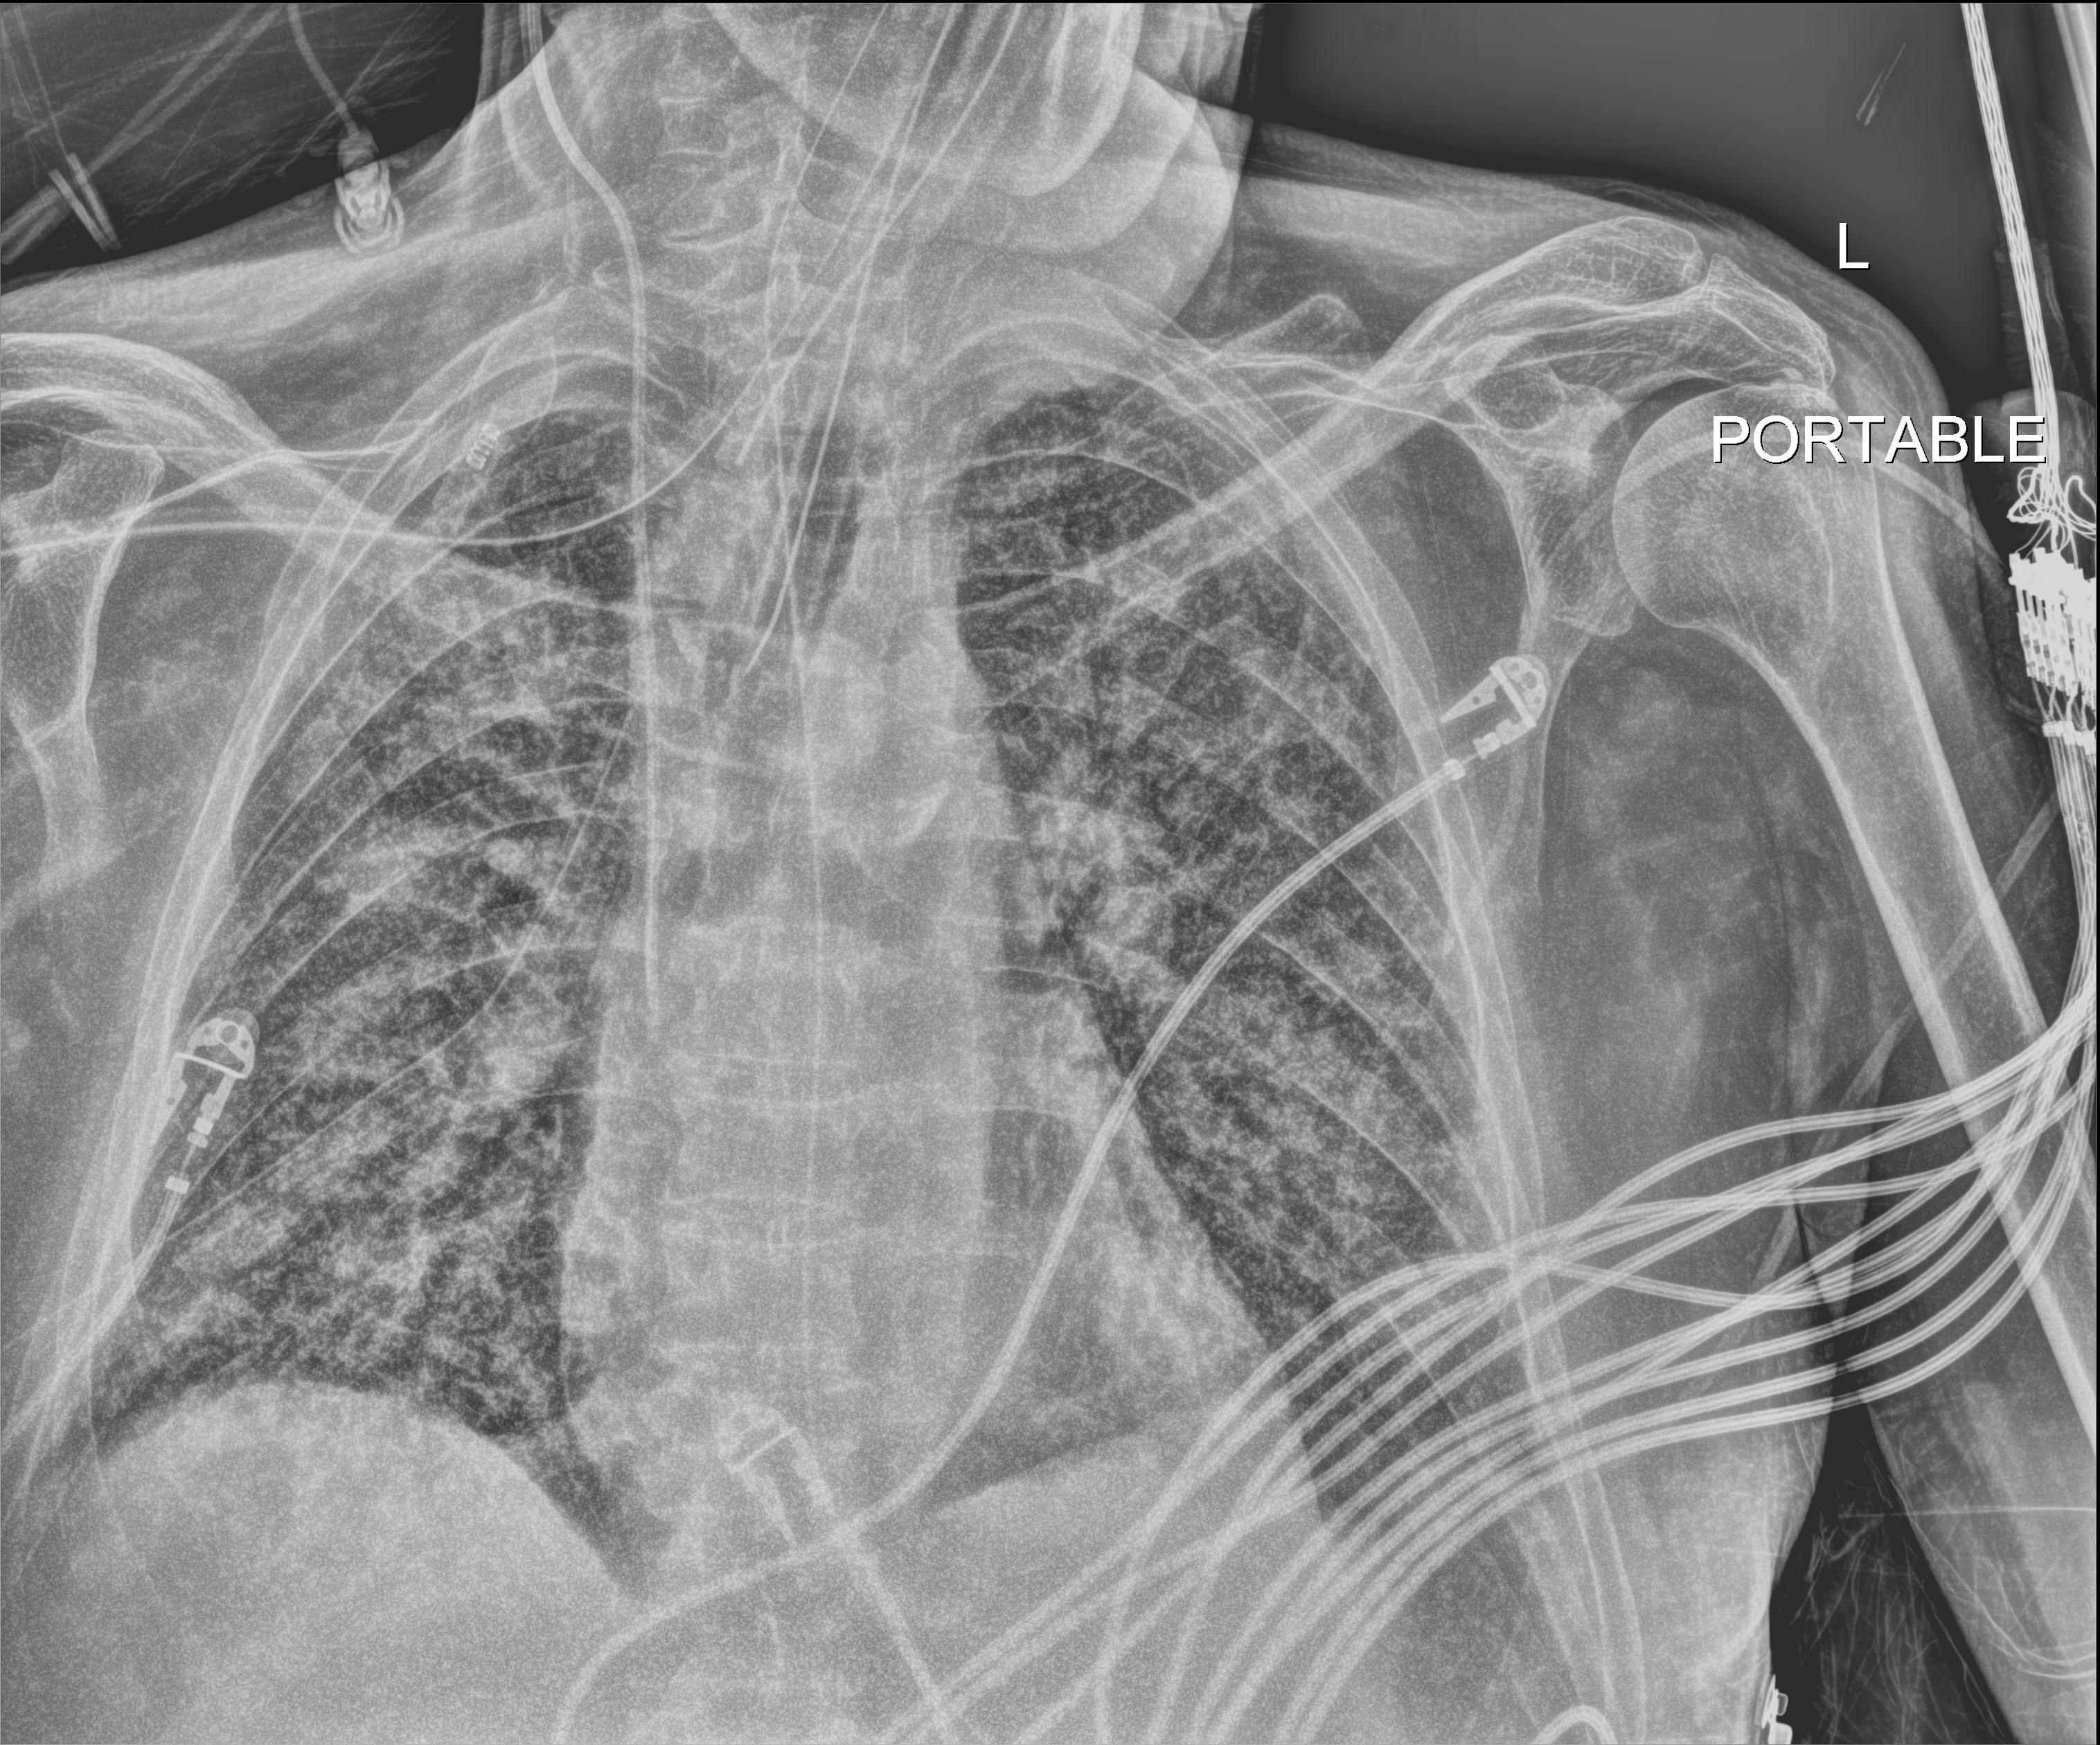
Chest X-ray (portable); anteroposterior (AP) projection. Male patient hospitalised with COVID-19, age 60–74 years.
Admission-level facts for this patient (not findings on this image; timing relative to this image not recorded): mechanically ventilated during this hospital stay: yes.